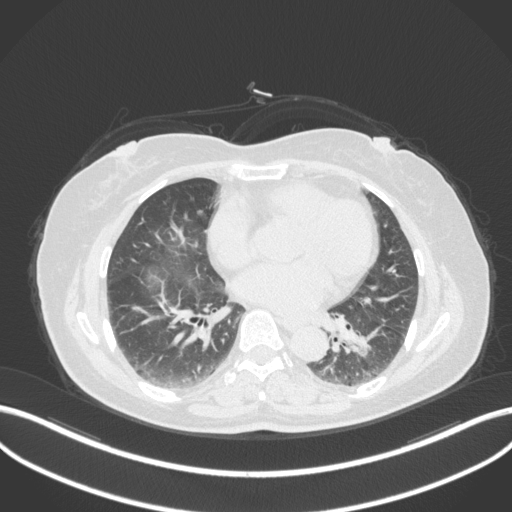
Chest CT, one axial slice. Slice 163 of 307 in the series (ordered by position). Reconstruction kernel B31f. Lung window (W 1500 / L -600 HU). 1 mm slice thickness. 512 × 512 image matrix, field of view 400 × 400 mm. Female patient, age 59 years. From the clinical record (not read from this slice): clinical TNM (as recorded): T2a N0 M0; histopathological grade: G2-3.
Outlined on this slice (rectangle marked by the reading radiologist):
- lung tumour (recorded histology: adenocarcinoma): bounding box [x1, y1, x2, y2] px = [347, 322, 386, 359]